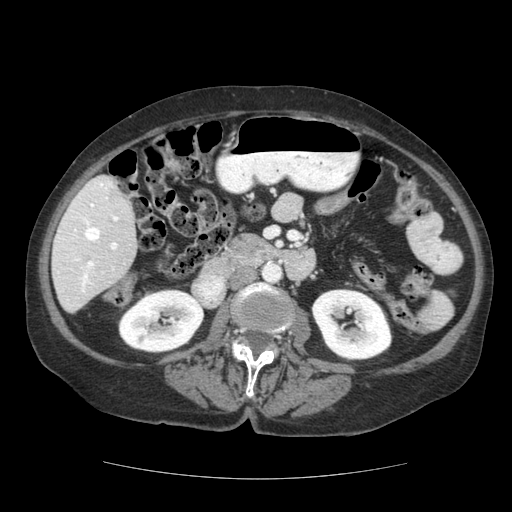
Contrast-enhanced abdominal CT (liver protocol), one axial slice. Position 50 of 111 along the scan axis. Reconstruction kernel STANDARD. Soft-tissue window (W 400 / L 40 HU). 512 × 512 image matrix, field of view 360 × 360 mm. From the clinical record (not read from this slice): diagnosis: hepatocellular carcinoma (patient treated with transarterial chemoembolisation; whether this scan precedes or follows treatment is not stated here); TNM stage (as recorded): Stage-I; Child-Pugh class: A; tumour differentiation: moderately-poorly differentiated; tumour nodularity: uninodular.
Structures marked on this image (semi-automatically segmented with operator editing):
- liver parenchyma outside the tumour (the mass and vessels are separate outlines, so this box may not span the whole liver): box from (x=52, y=174) to (x=136, y=312) px
- liver vessels: (x=58, y=181)–(x=119, y=292)